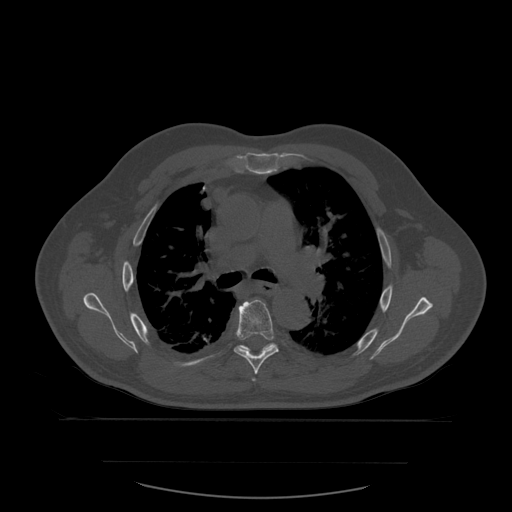
CT including the spine, one axial slice; slice 402 of 590 in the series (ordered by position); bone window (W 1800 / L 400 HU); 512 × 512 image matrix. Patient age 71 years. Case-level facts recorded for this patient, not image findings: primary cancer: lung; vertebrae with lytic lesions (as recorded): T1, T2, L5, S1.
Annotated regions visible in this slice (semi-automatic segmentation, software-assisted and operator-edited):
- T5 vertebra: box from (x=253, y=378) to (x=256, y=382) px
- T6 vertebra: (x=234, y=300)–(x=279, y=375)
- T7 vertebra: (x=239, y=343)–(x=276, y=353)